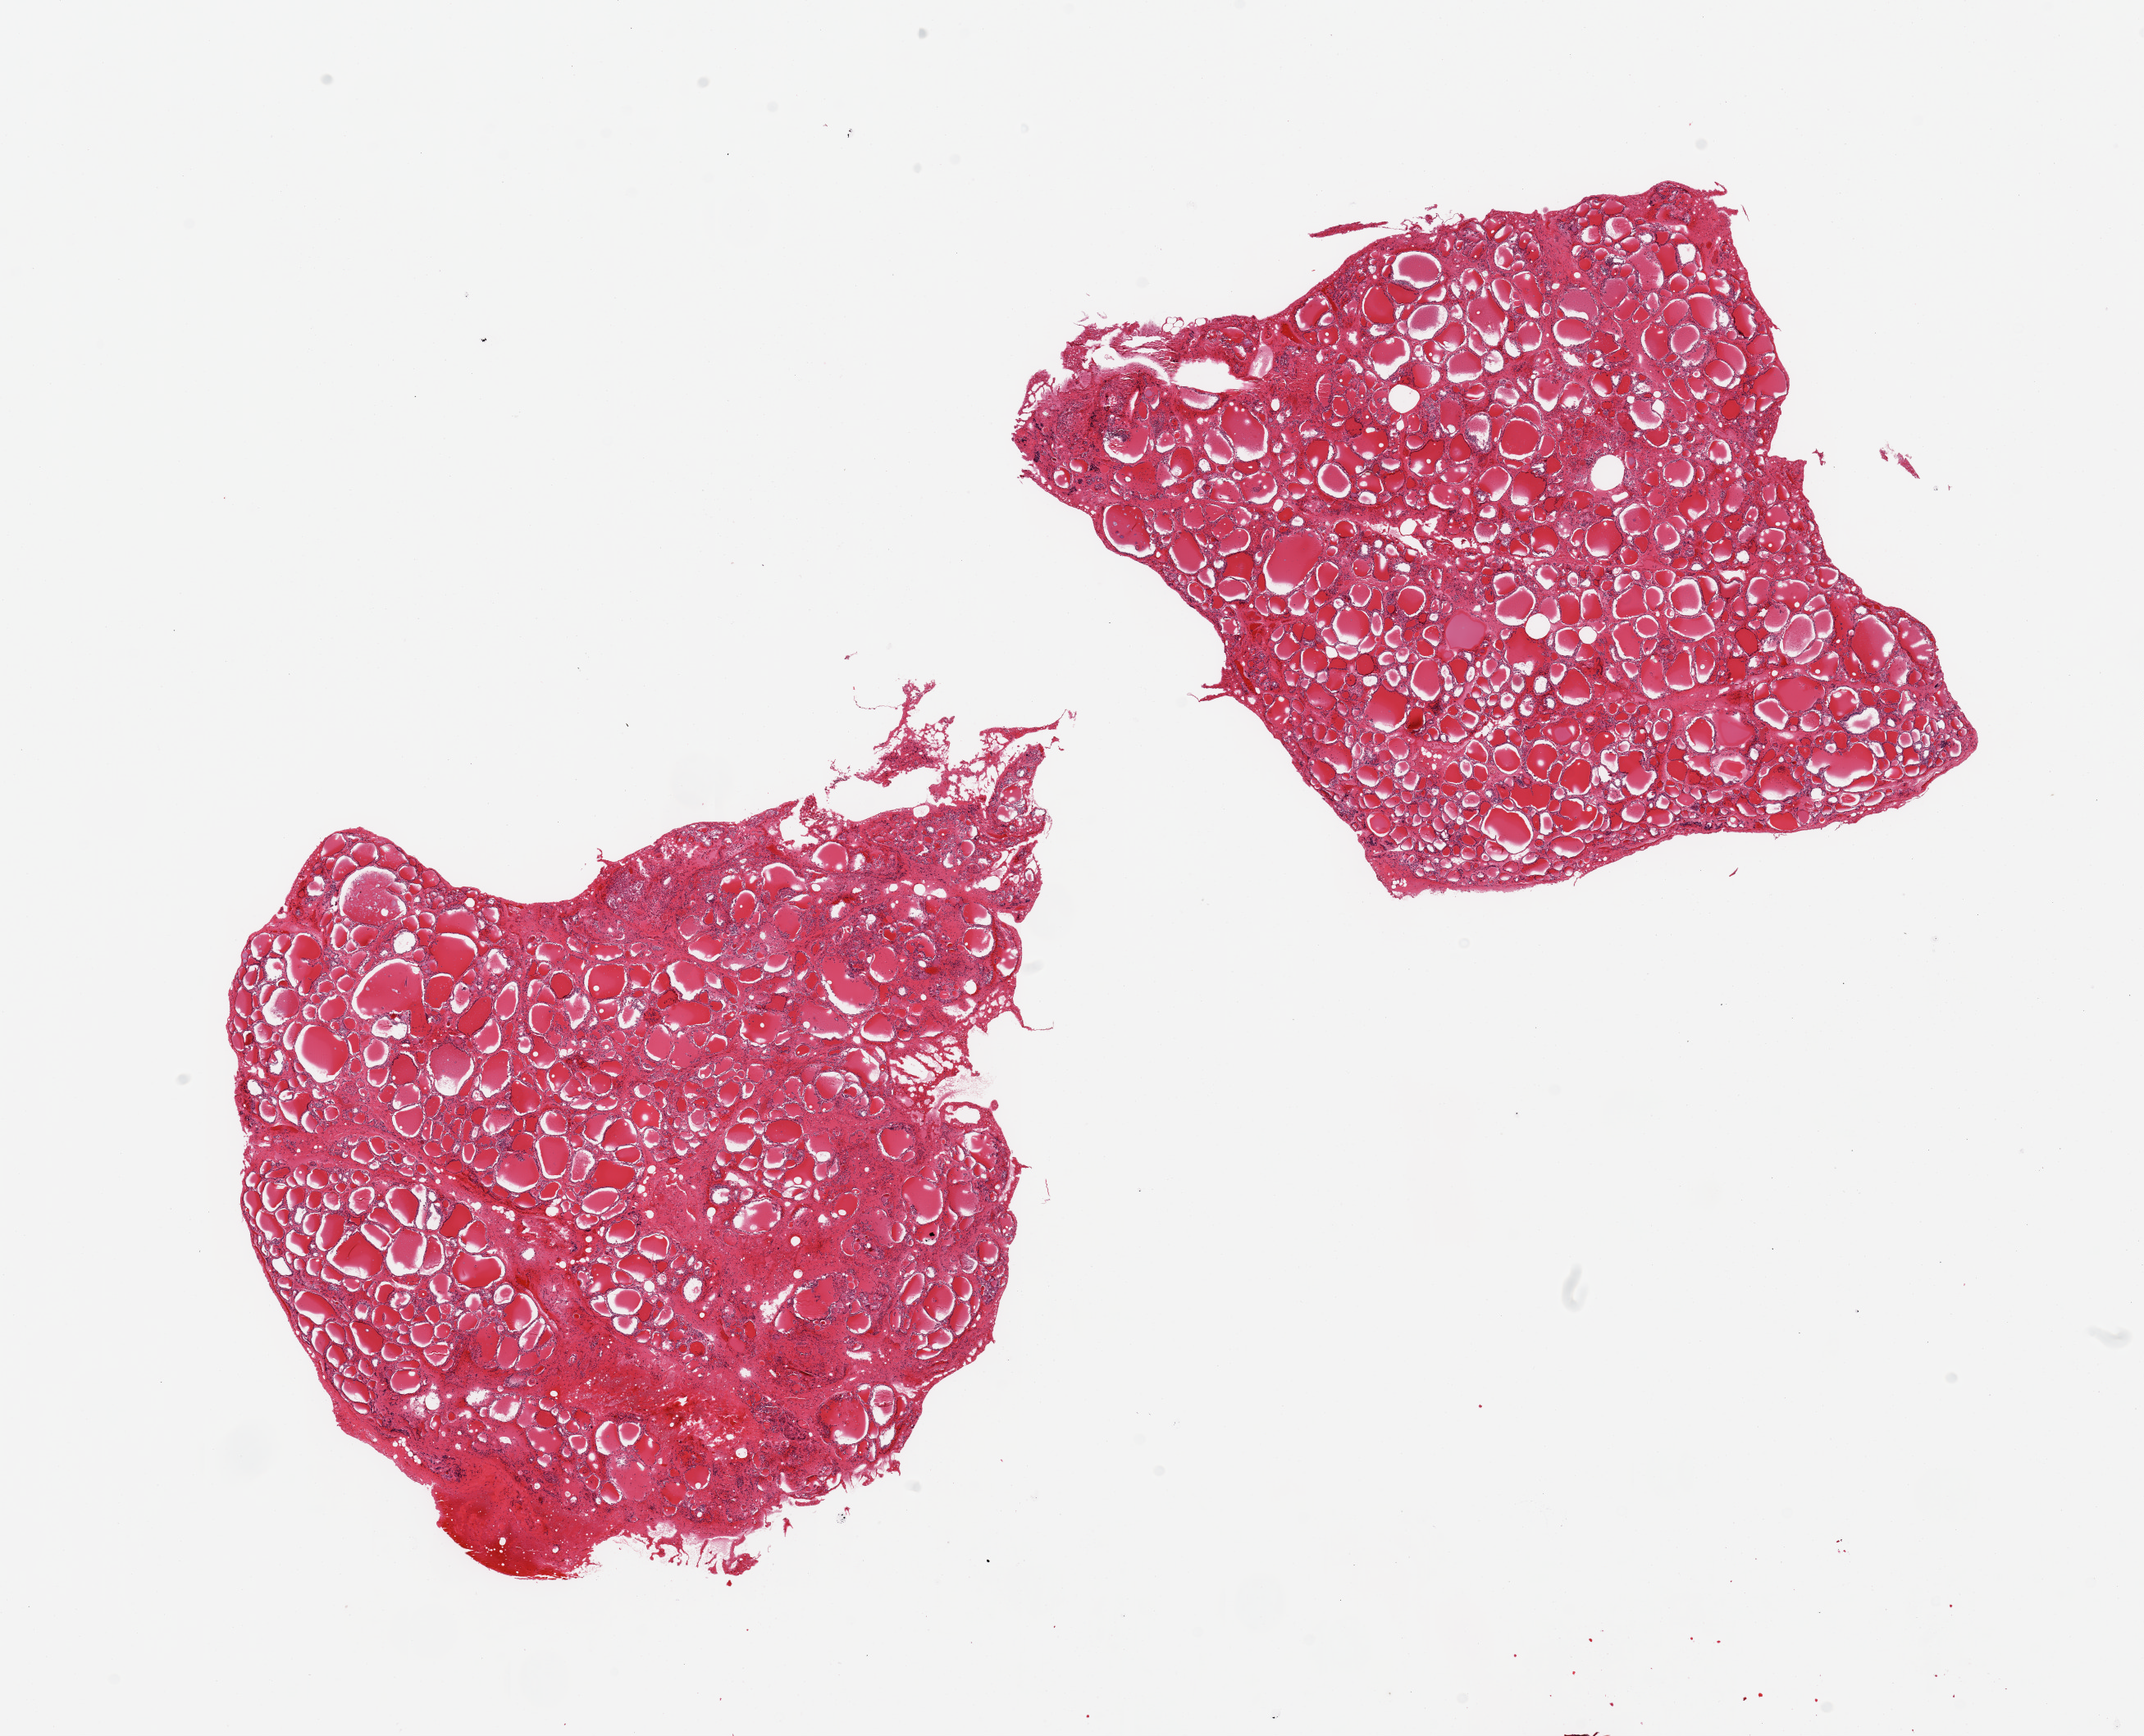
Whole-slide image, haematoxylin and eosin stain, a low-resolution overview of the entire scanned area, about 20.7 x 16.7 mm (acquisition: 20x scan), PAXgene-fixed, paraffin-embedded tissue, sampled site (target tissue): thyroid, donor tissue sample. Female donor.
* review note (as recorded): 2 pieces